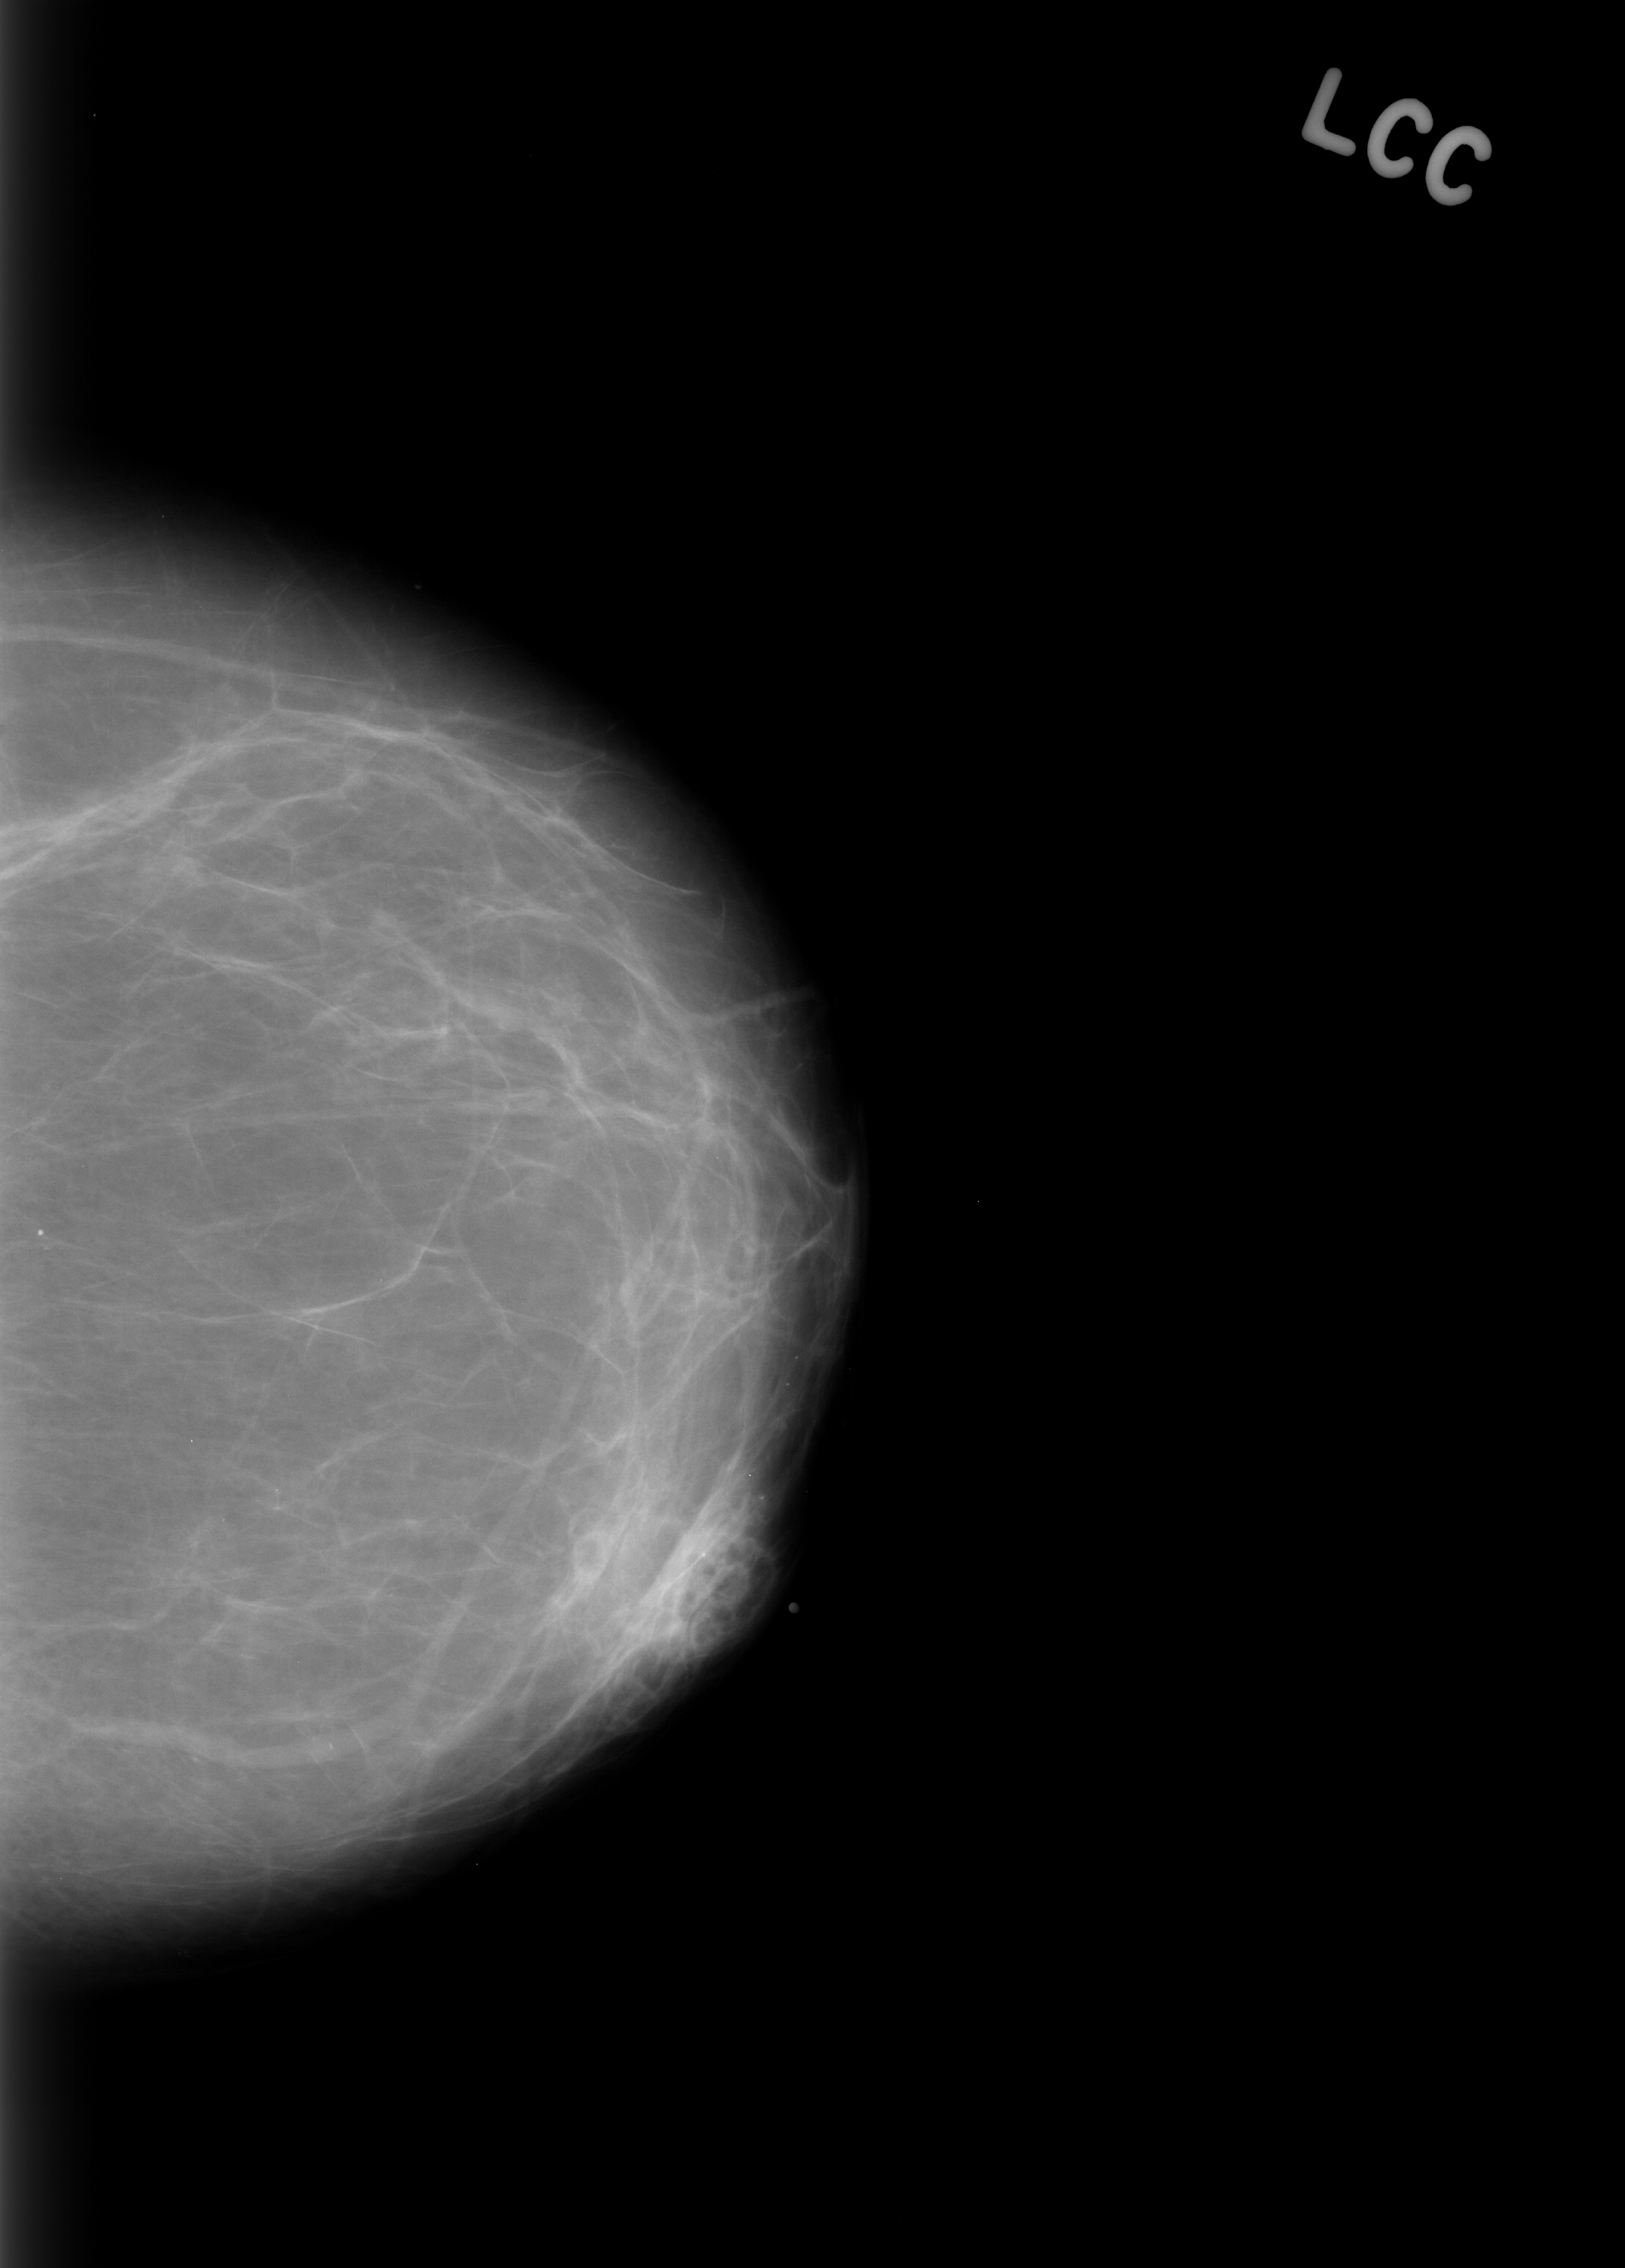
Digitized screen-film mammogram, left breast, craniocaudal (CC) view, BI-RADS breast density category 1 (scale 1–4).
Mass, shape focal asymmetric density, margins ill defined; BI-RADS assessment category 3; pathology (as recorded): benign.